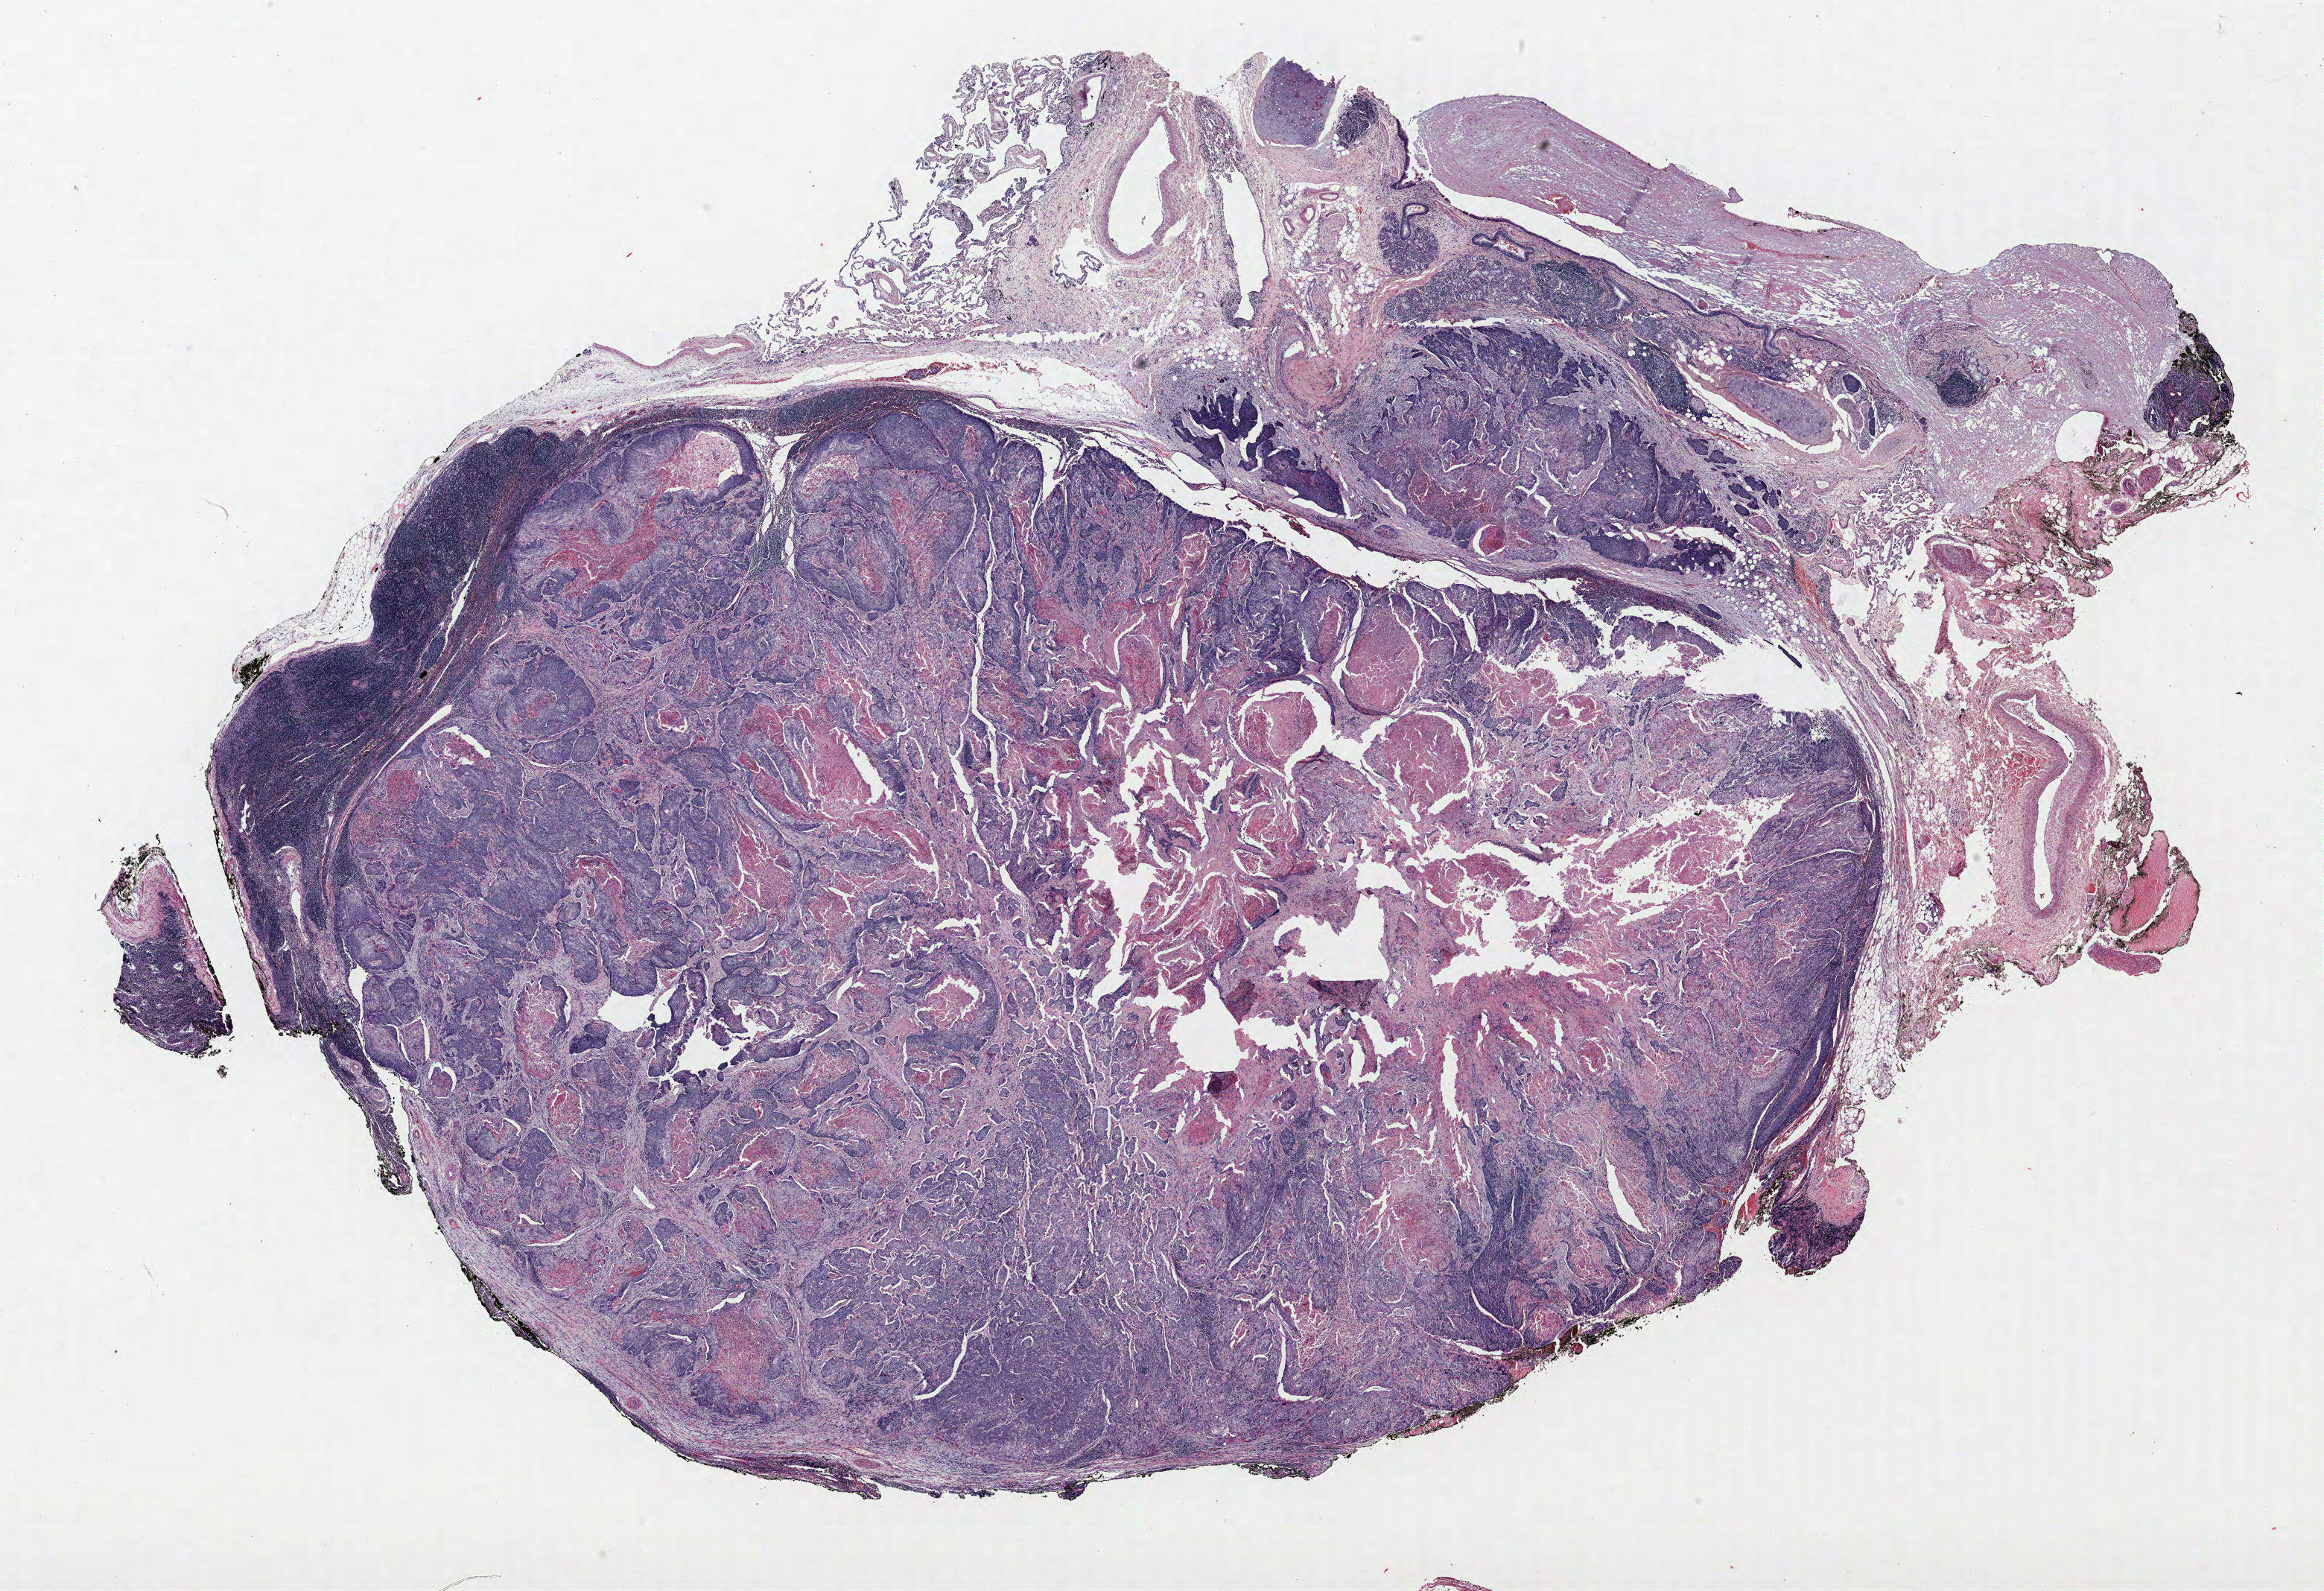
Hematoxylin and eosin (H&E) stained whole-slide image, whole scanned area (about 25.0 x 17.1 mm, from a 40x scan) shown as a low-resolution overview, formalin-fixed paraffin-embedded (FFPE) section, lung. Female patient, aged 63 at enrolment. Former smoker at enrolment.
Participant's lung-cancer diagnosis: Squamous cell carcinoma, keratinizing, NOS (ICD-O-3 8071/3).